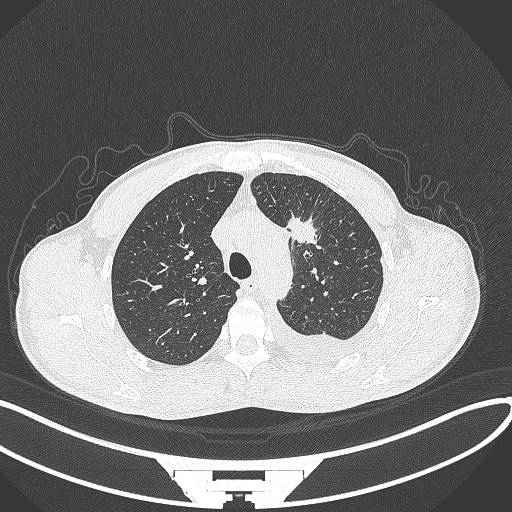
Chest CT, one axial slice; slice 252 of 371 in the series (ordered by position); reconstruction kernel B70f; lung window (W 1500 / L -600 HU); 1 mm slice thickness; 512 × 512 image matrix, field of view 400 × 400 mm. Patient: male, 49 years. From the clinical record (not read from this slice): clinical TNM (as recorded): T1c N1 M1.
Outlined on this slice (bounding box drawn by a radiologist):
- lung tumour (recorded histology: adenocarcinoma): bounding box (x1, y1, x2, y2) in pixels: (283, 204, 322, 247)